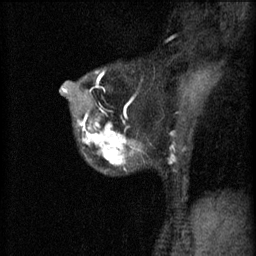
Breast MRI (dynamic contrast-enhanced), one sagittal slice. Position 41 of 60 along the scan axis. 3 images stored at this slice position (order not interpretable as contrast timing). 1.5 T. TE 4.2 ms, TR 11 ms. 2 mm slice thickness. 256 × 256 image matrix. Female patient, age 37 years.
Outlined on this slice (semi-automatically segmented with operator editing):
- analysis volume of interest (the breast-tissue region the enhancement analysis was run in; not a lesion): bounding box <74,118,176,173> (left, top, right, bottom; pixels)
- tumour enhancement mask (voxels above the 70 % enhancement threshold inside the analysis volume of interest): <77,118,175,165>